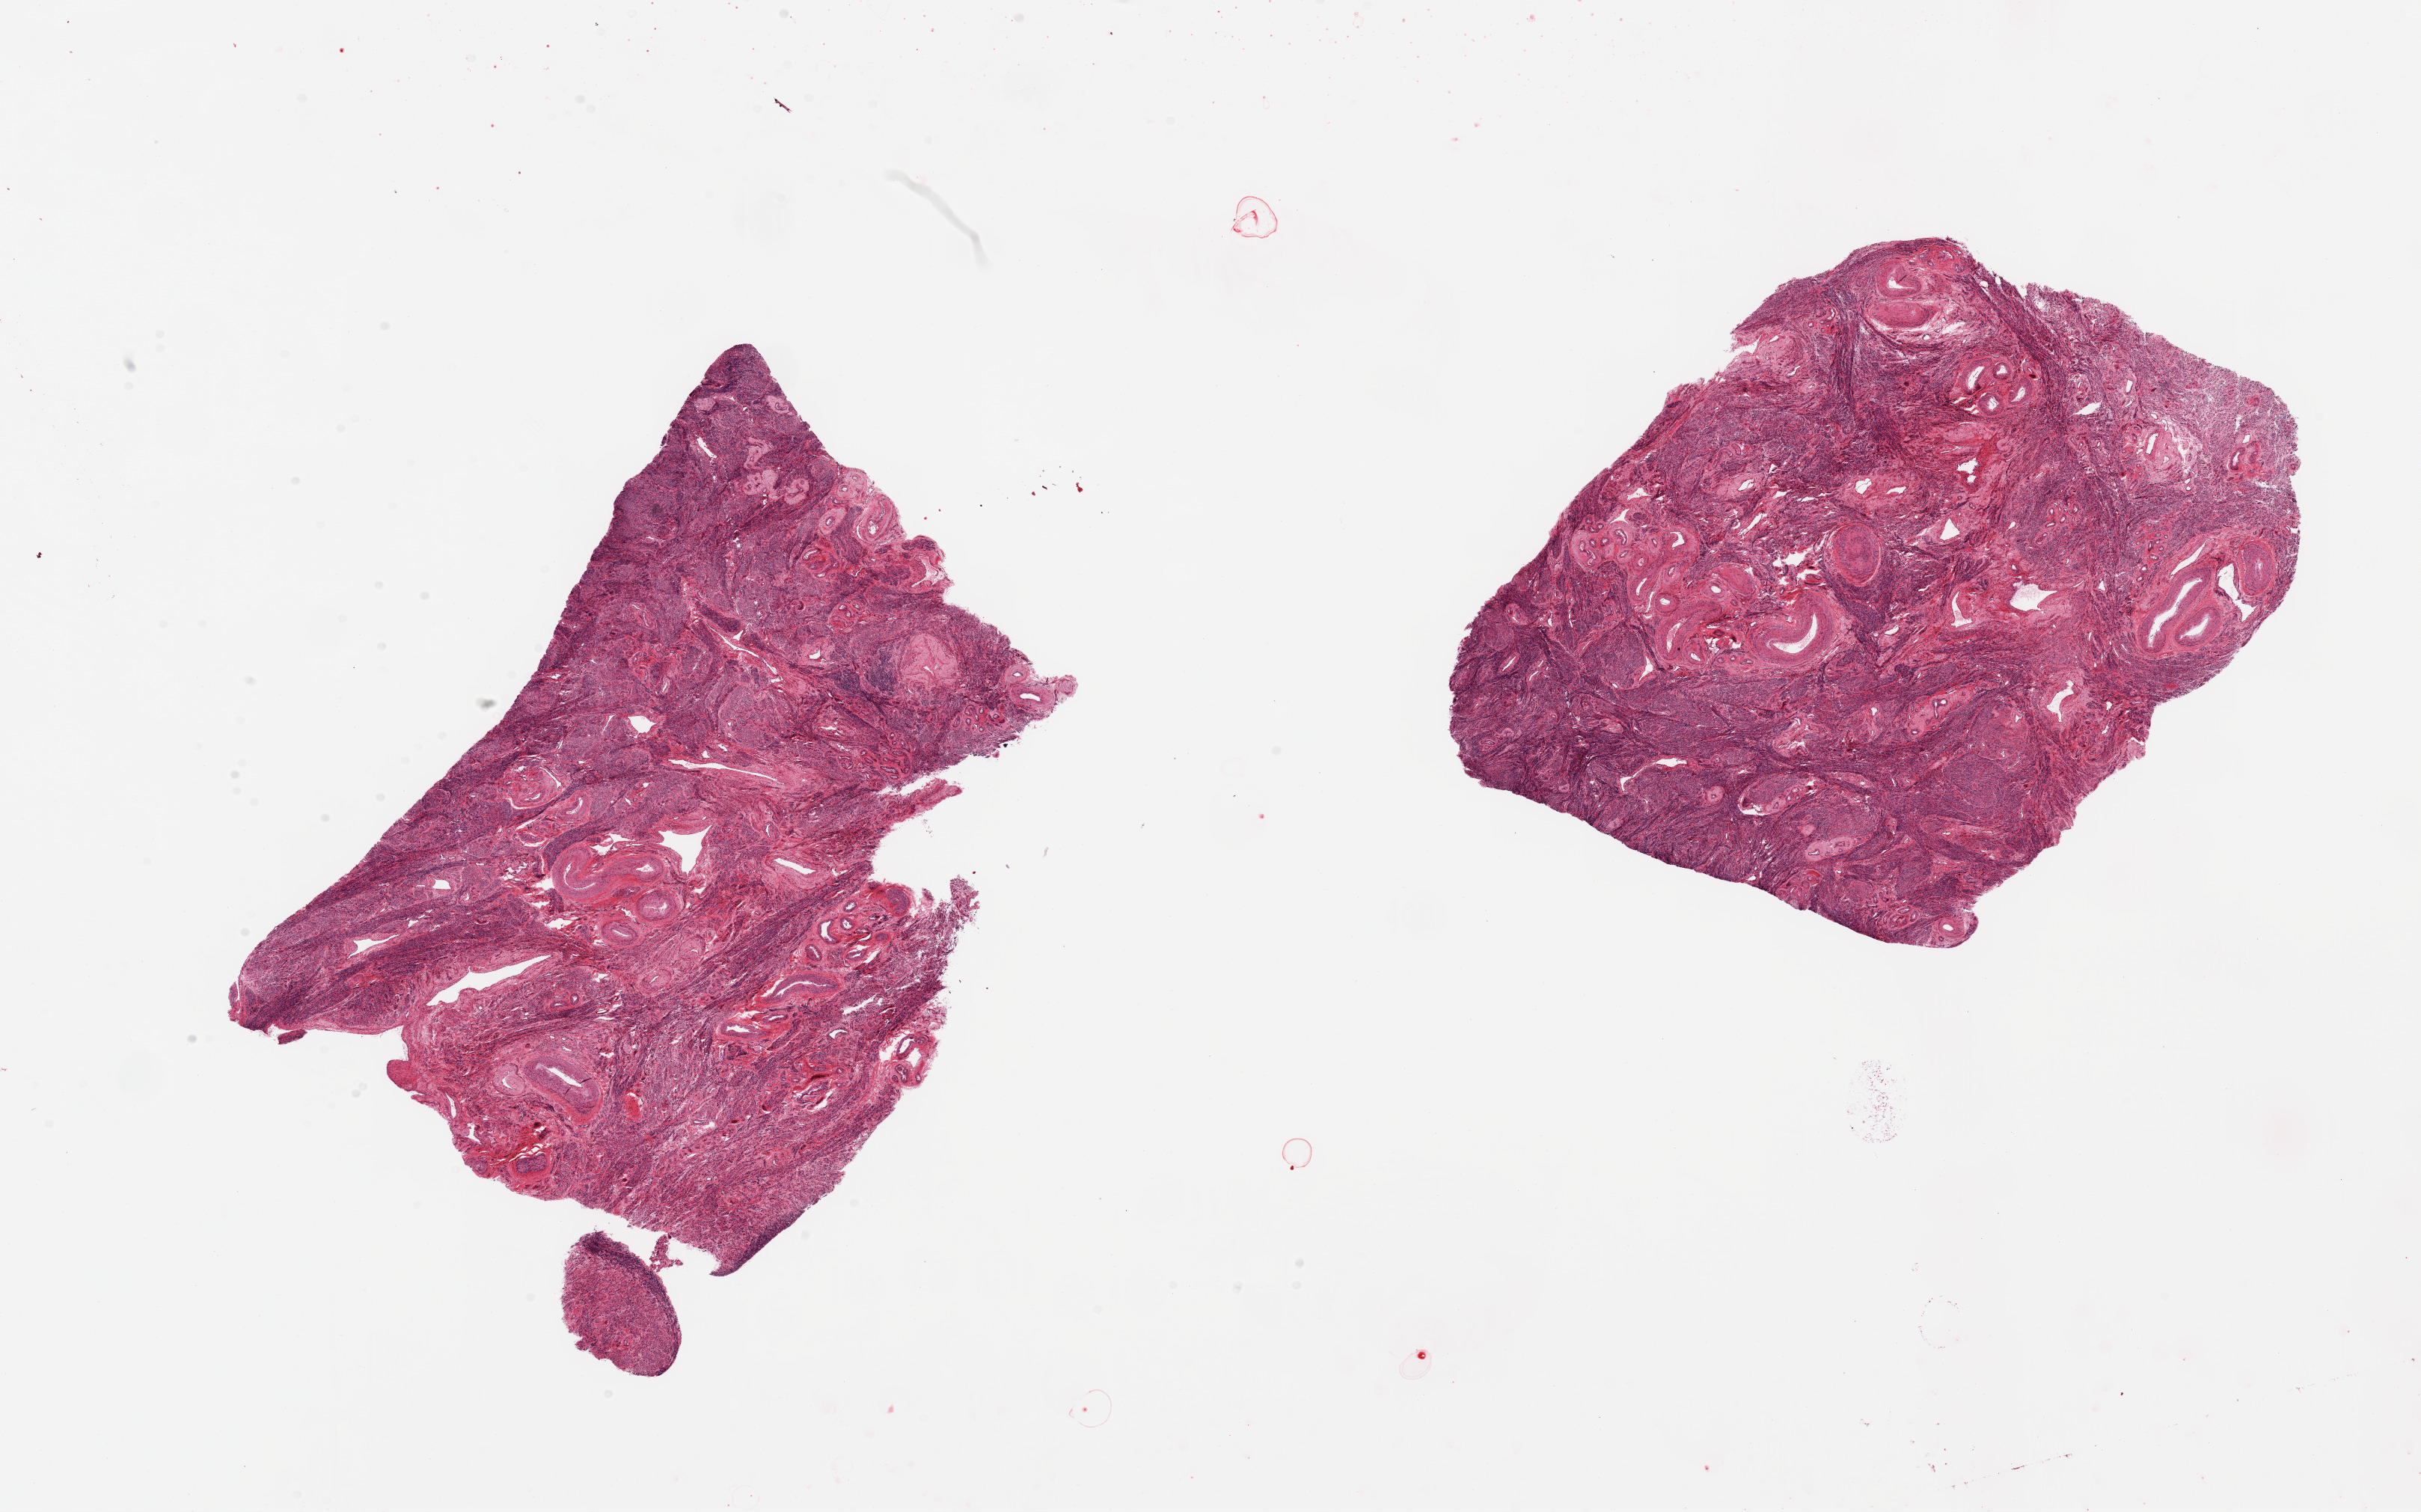
Digitized hematoxylin and eosin (H&E)-stained section, low-resolution overview of the scanned area, about 25.6 x 16.0 mm; PAXgene-fixed paraffin-embedded (PFPE) section; target tissue: uterus; donor tissue sample. Donor sex: female.
Review note (as recorded): 2 pieces; myometrium with prominent vascular component; no endometrium in these cuts.